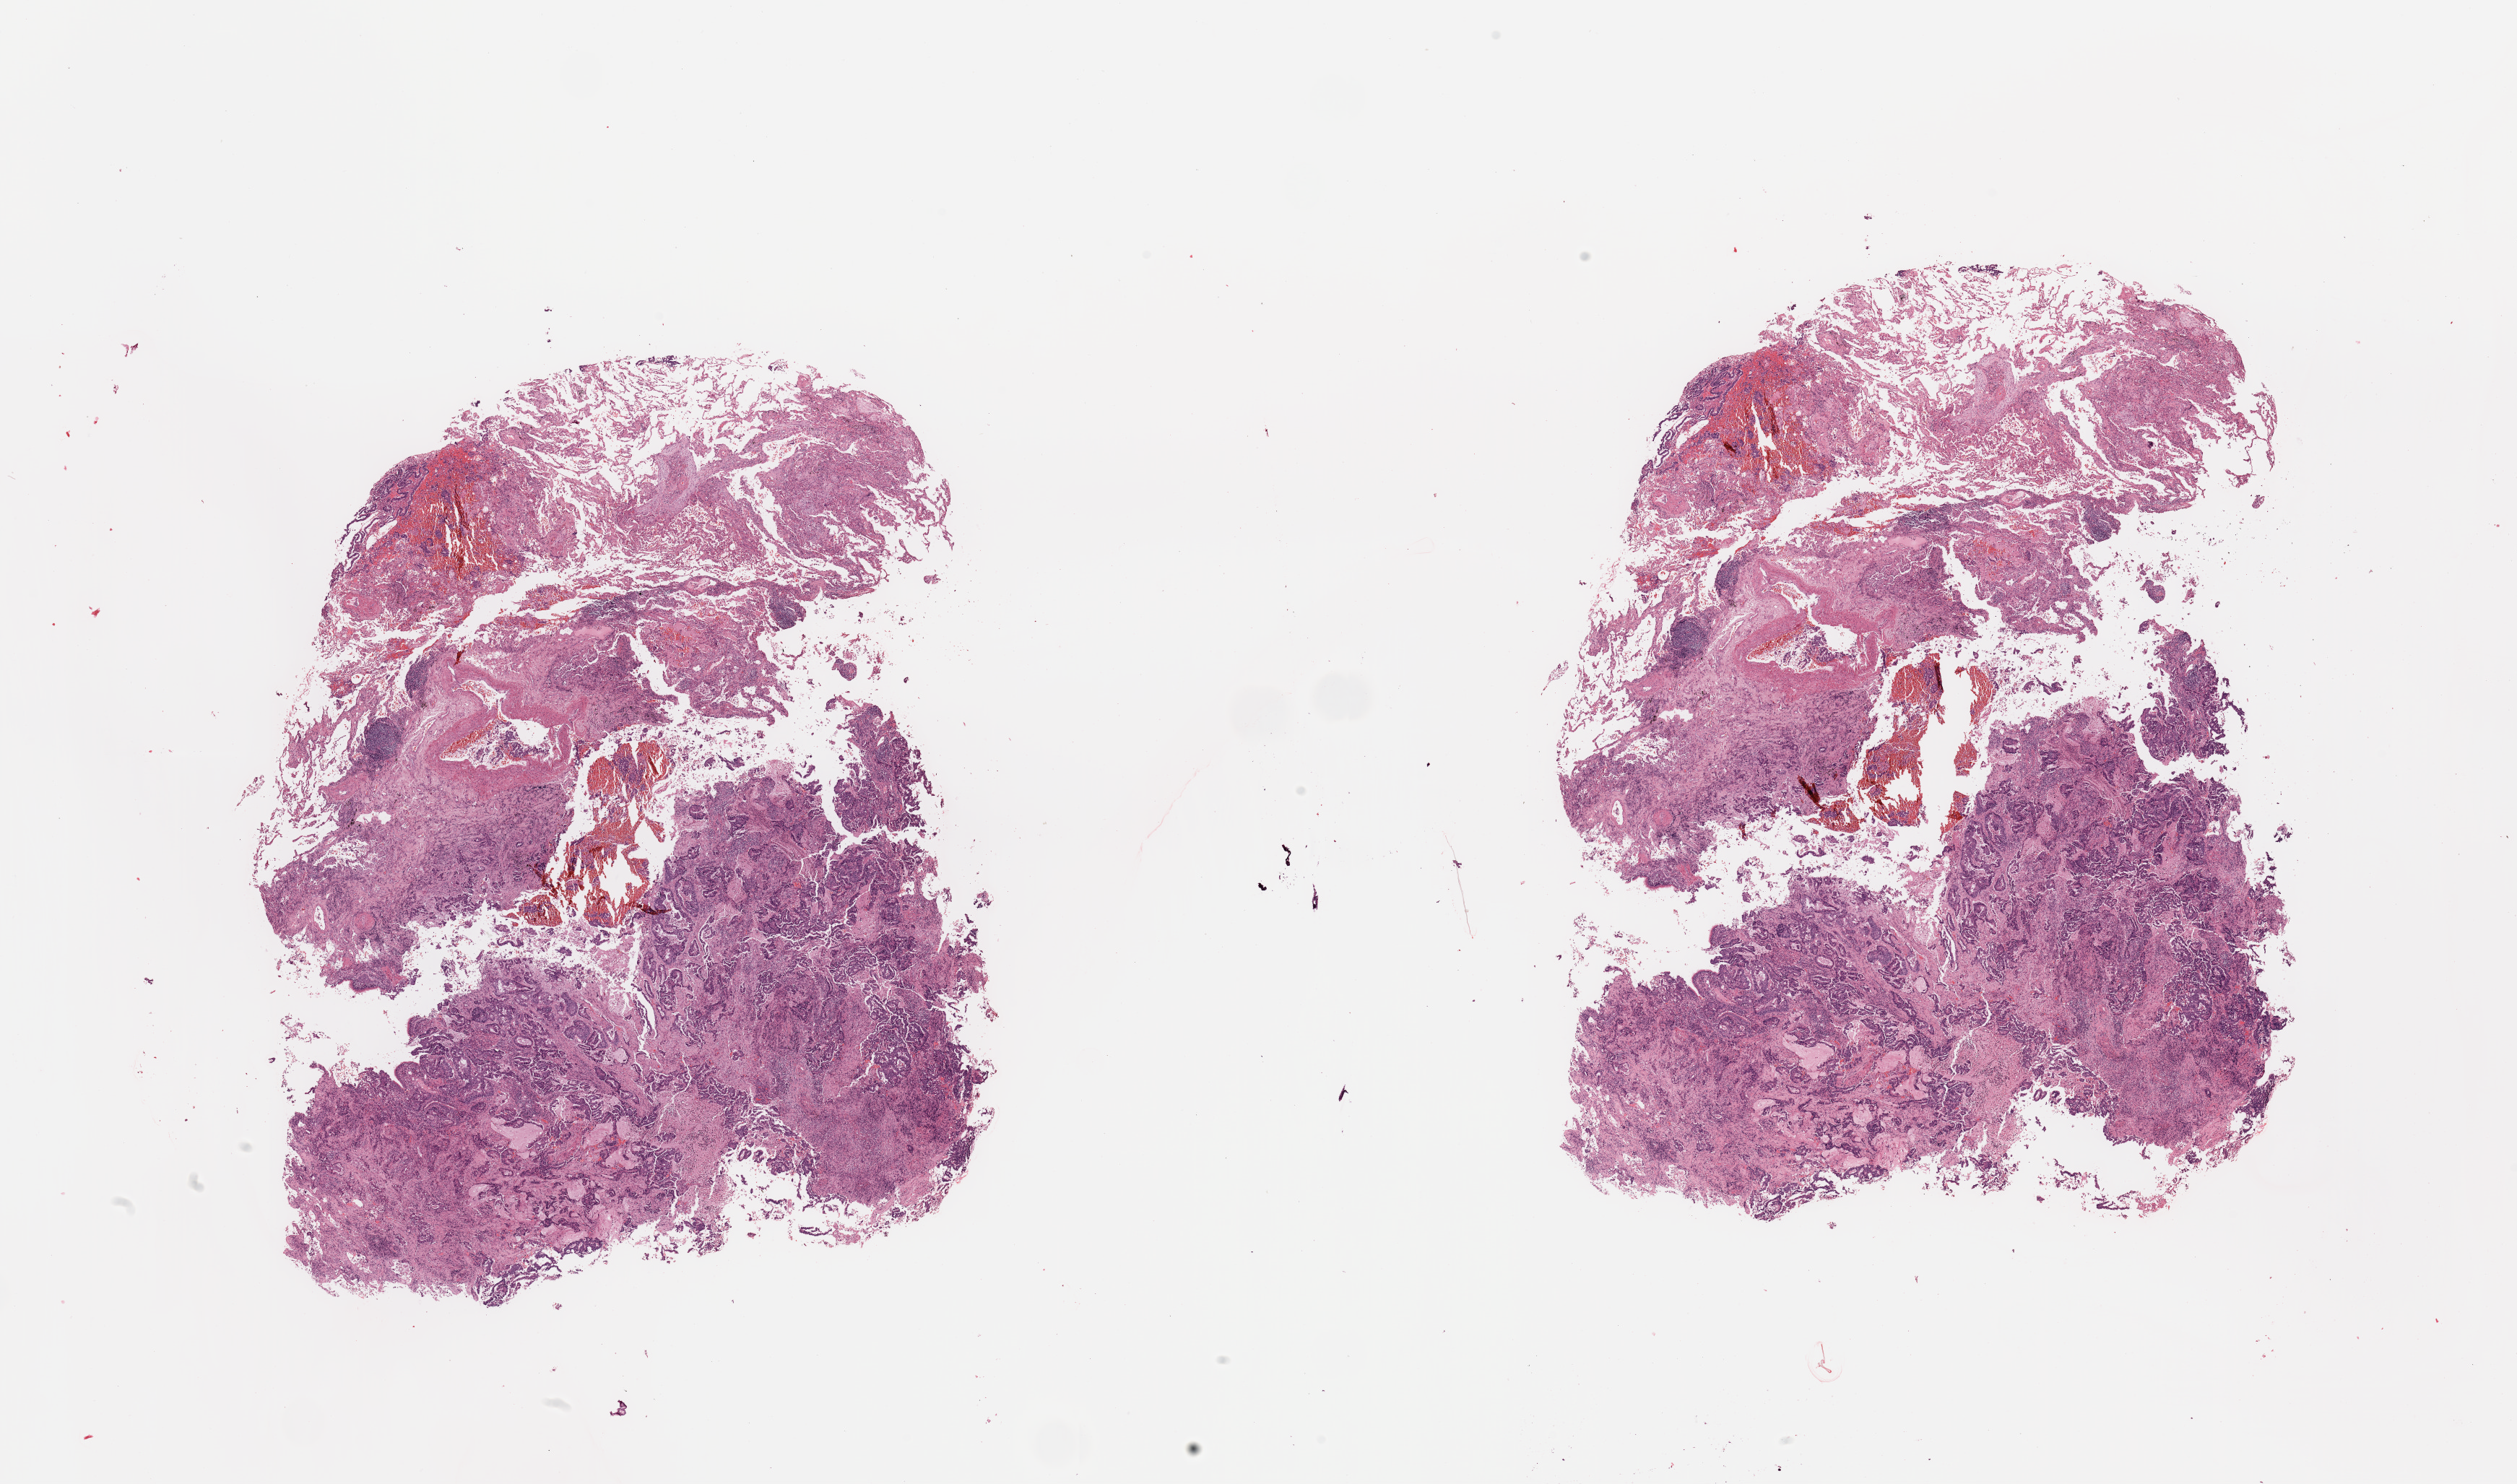
H&E-stained whole-slide image, shown as a low-resolution overview of the whole scanned area (about 27.6 x 16.3 mm, slide scanned at 20x). Tumour tissue sample, lung. Male, 63 y/o. Histologic grade: G2 (moderately differentiated).
- histologic diagnosis: Adenocarcinoma, NOS
- AJCC pathologic stage: IIA
- primary tumour site (as recorded): right middle lobe